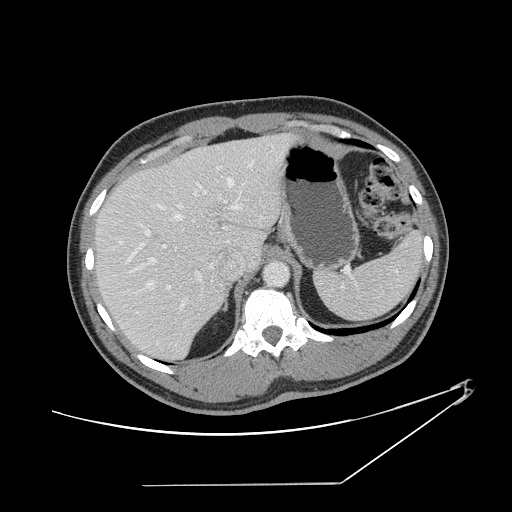
Contrast-enhanced abdominal CT, one axial slice. Slice 104 of 152 in the series (ordered by position). Reconstruction kernel STANDARD. 120 kVp. Intravenous contrast given. Soft-tissue window (W 400 / L 40 HU). 512 × 512 image matrix, field of view 432 × 432 mm. Male patient, age 45 years. Case-level facts recorded for this patient, not image findings: diagnosis: colorectal cancer liver metastases, imaged before liver resection; multiple liver metastases: no; largest metastasis: 1 cm; chemotherapy before resection: yes.
Annotated regions visible in this slice (manually delineated by an expert):
- hepatic veins: bounding box [x1, y1, x2, y2] px = [111, 160, 255, 310]
- liver: [97, 136, 292, 360]
- planned liver remnant (the part of the liver to remain after resection): [97, 154, 233, 360]
- portal vein (with intrahepatic branches): [138, 184, 241, 343]